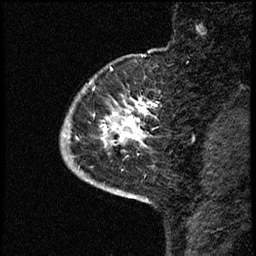
Breast MRI (dynamic contrast-enhanced), one sagittal slice. Slice 10 of 68 in the series (ordered by position). Dynamic contrast-enhanced study with each time point stored as its own series, time point 2 of 3 at this slice position (early post-contrast, ordered by acquisition time). 1.5 T. TE 4.2 ms, TR 17.6 ms. 2 mm slice thickness. 256 × 256 image matrix, field of view 200 × 200 mm. Patient: female, 52 years. From the clinical record (not read from this slice): setting: breast cancer imaged before/during neoadjuvant chemotherapy; receptor status: HER2-positive.
Outlined on this slice (semi-automatic segmentation, software-assisted and operator-edited):
- analysis volume of interest (the breast-tissue region the enhancement analysis was run in; not a lesion): bounding box <61,61,175,184> (left, top, right, bottom; pixels)
- tumour enhancement mask (voxels above the 100 % enhancement threshold inside the analysis volume of interest): <66,101,146,148>